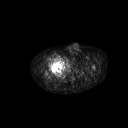
FDG PET of an extremity soft-tissue mass (from a PET/CT study), one axial slice. Slice 286 of 311 in the series (ordered by position). 128 × 128 image matrix, field of view 700 × 700 mm. Patient: male, 50 years. Case-level facts recorded for this patient, not image findings: histological type: undifferentiated - pleiomorphic; grade: high; site of the primary tumour: right thigh.
Annotated regions visible in this slice (expert contour drawn on MRI and transferred to this co-registered scan by the dataset authors):
- gross tumour volume including surrounding oedema: bounding box (x1, y1, x2, y2) in pixels: (53, 54, 65, 67)
- gross tumour volume (mass): (53, 56, 64, 66)